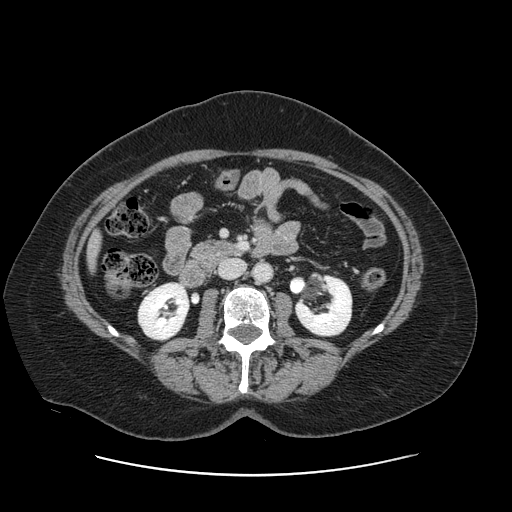
Contrast-enhanced abdominal CT, one axial slice; intravenous contrast given; soft-tissue window (W 400 / L 40 HU); 512 × 512 image matrix, field of view 398 × 398 mm. Female patient, age 62 years. From the clinical record (not read from this slice): diagnosis: colorectal cancer liver metastases, imaged before liver resection; multiple liver metastases: no.
Annotated regions visible in this slice (manually delineated by an expert):
- liver: box from (x=90, y=240) to (x=98, y=262) px